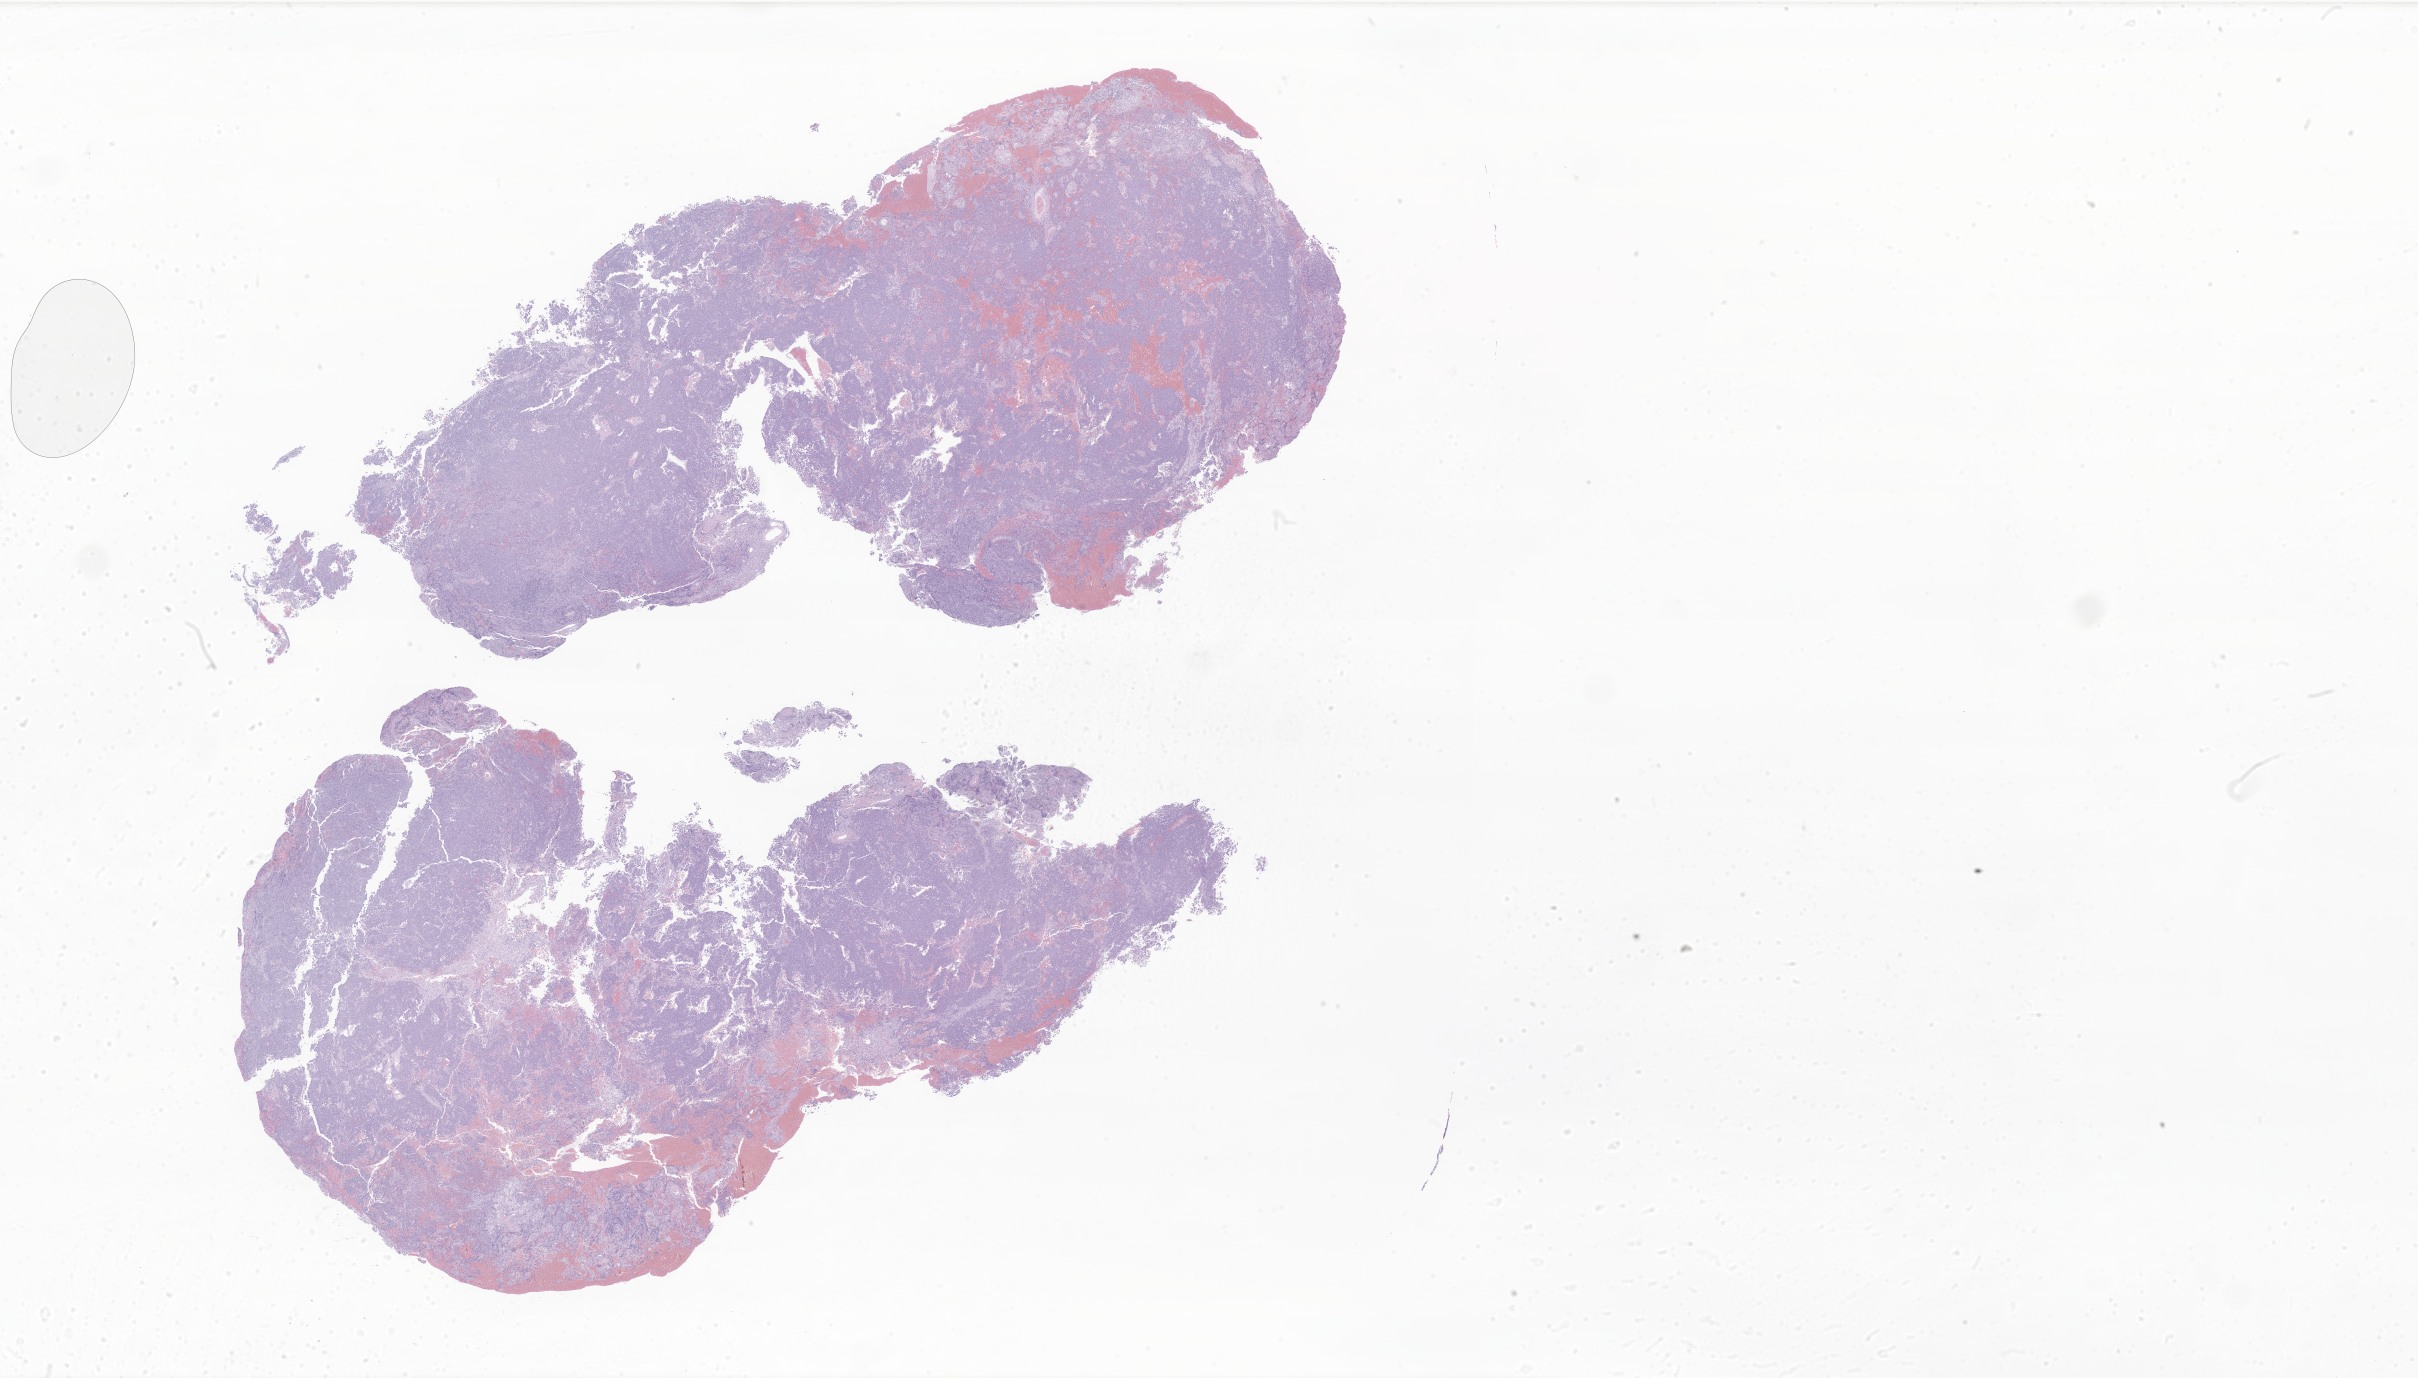
Digitized H&E-stained section of tumor tissue from the cerebral ventricle — a low-resolution overview of the entire scanned area, about 40.8 x 23.2 mm. Formalin-fixed, paraffin-embedded (FFPE) tissue. Female patient, age 143 months (11 years 11 months).
Diagnosis: Germinoma.